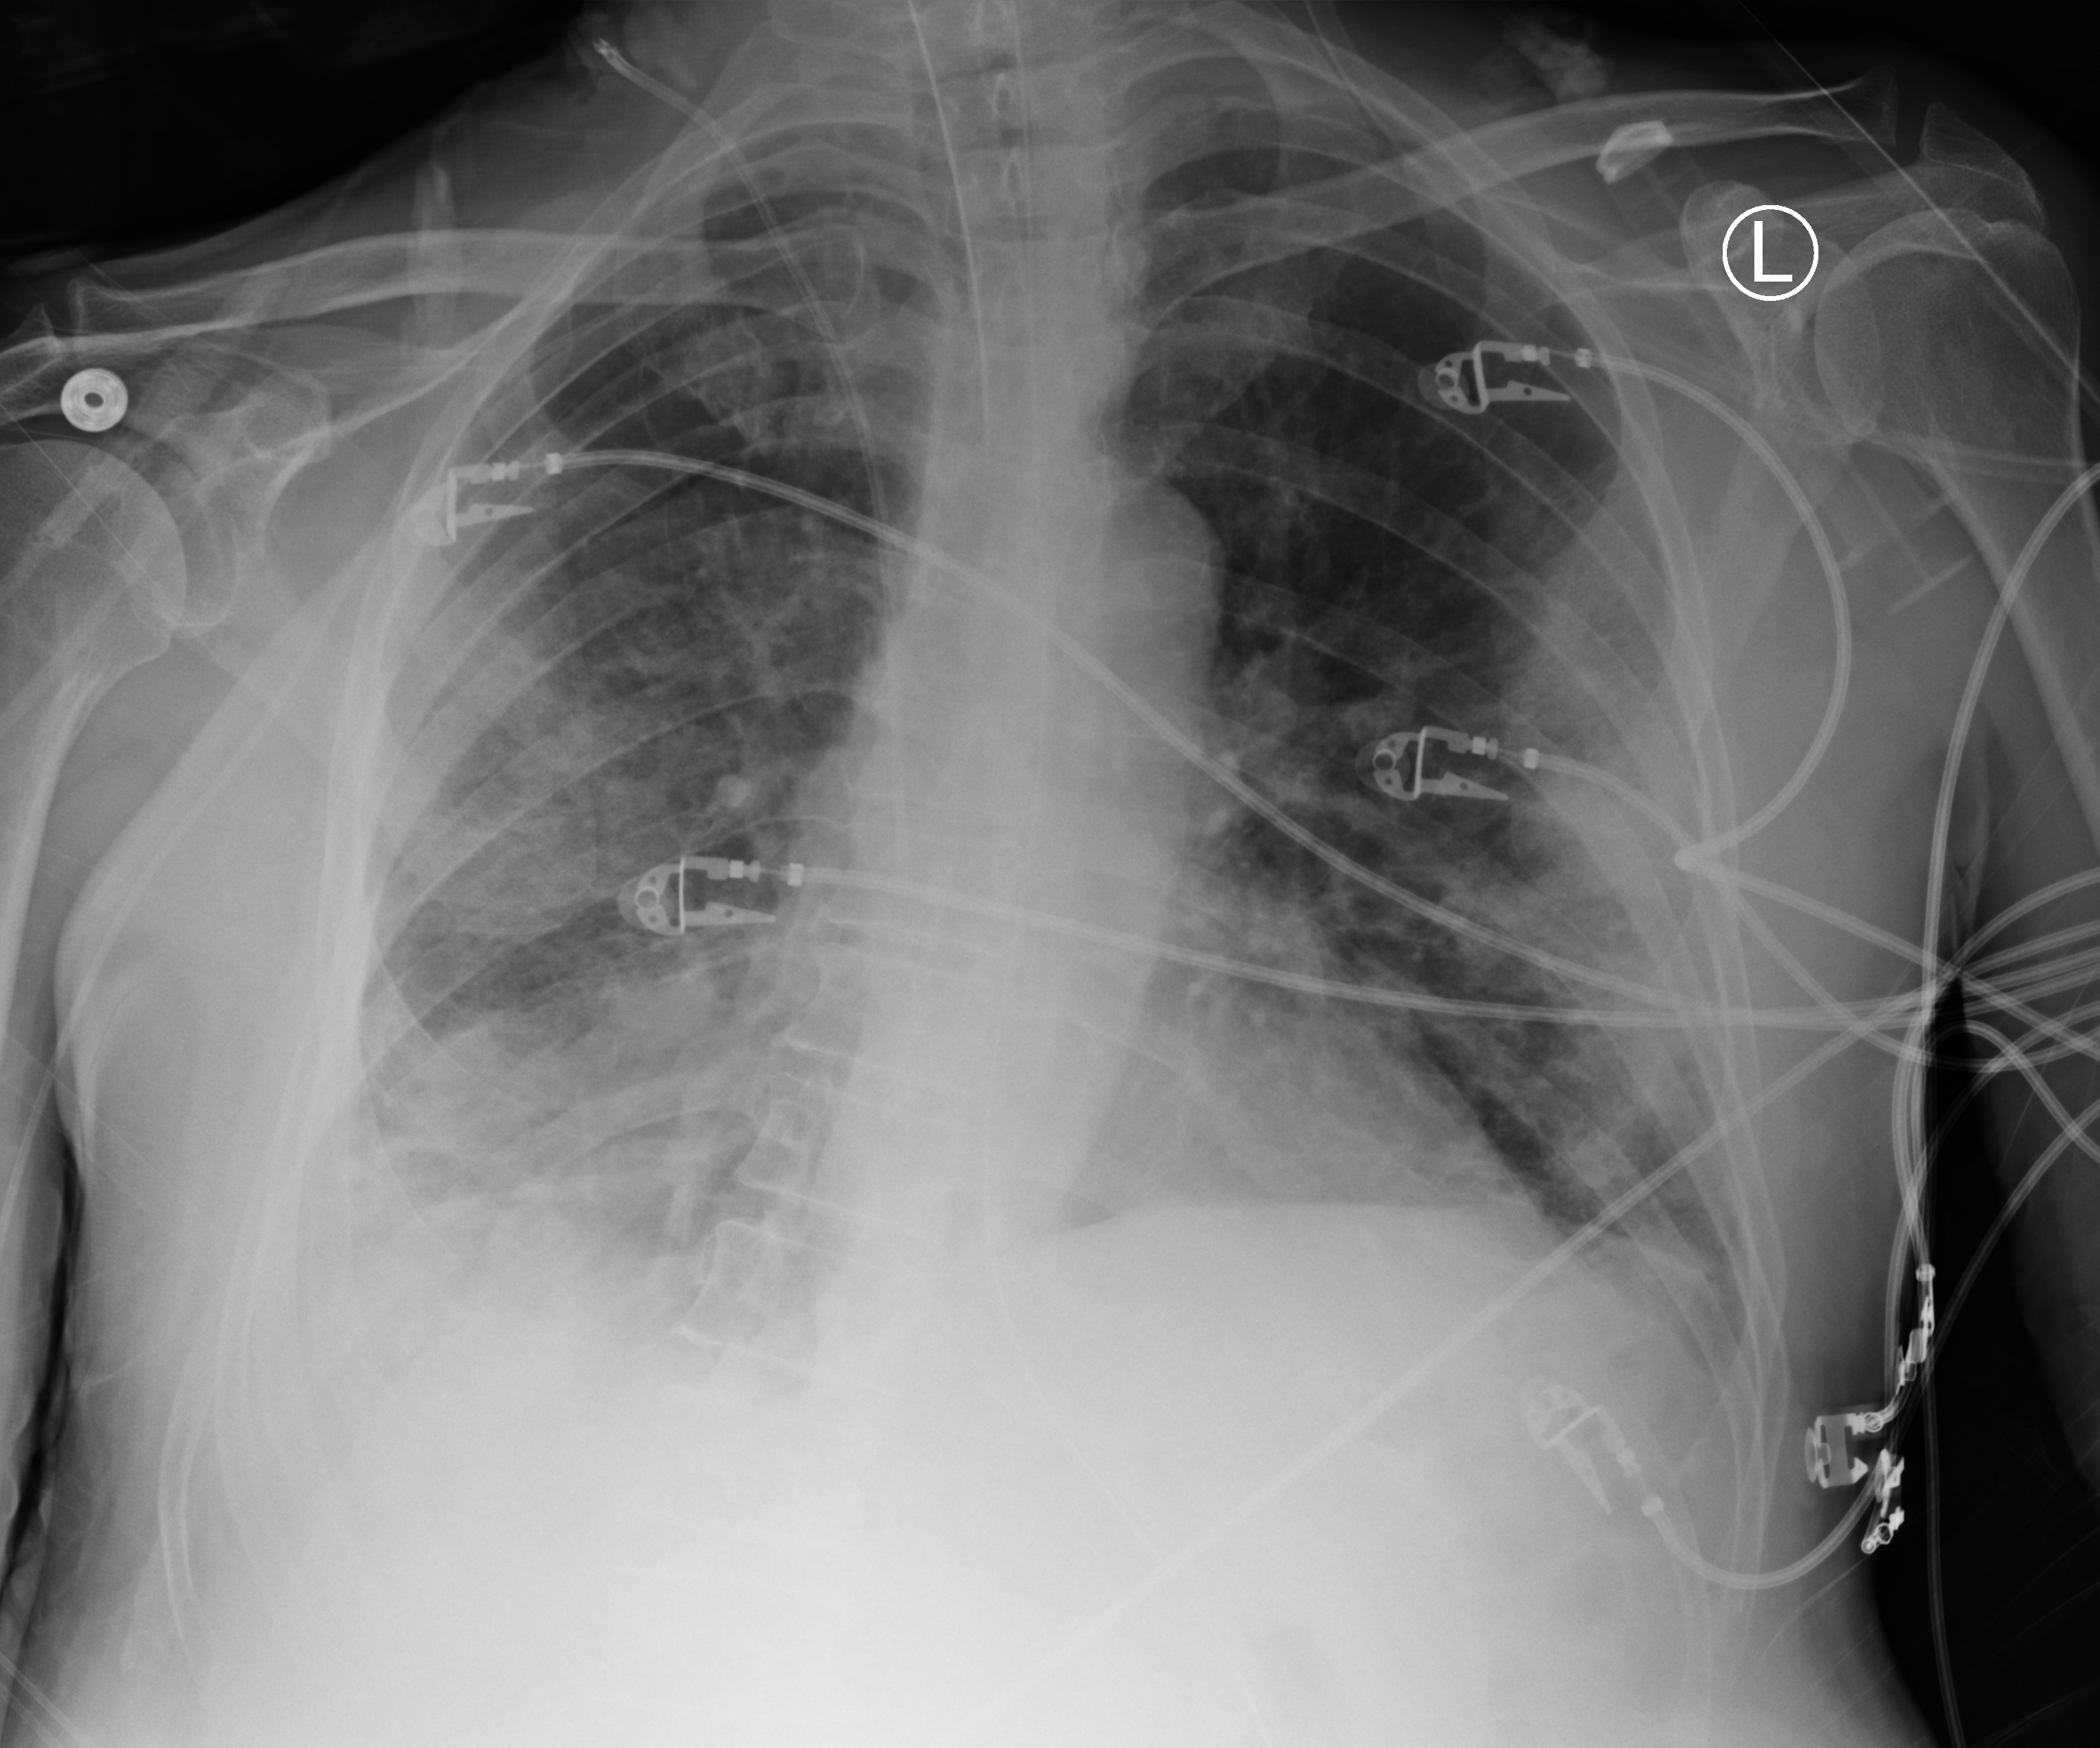
Portable chest radiograph; anteroposterior (AP) projection. Patient hospitalised with COVID-19; male, aged 75–90 years.
From the hospital-stay record, not from the radiograph (when in the stay this image was taken is not recorded): admitted to intensive care during this hospital stay: yes; length of hospital stay: 70 days.